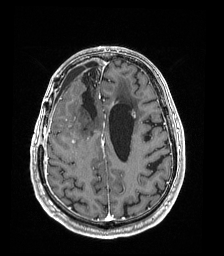
Brain MRI from a brain-tumour surgery series, one axial slice. Position 61 of 192 along the scan axis. T1-weighted post-contrast. 1 mm slice thickness. 224 × 256 image matrix. Case-level facts recorded for this patient, not image findings: histopathology: Astrocytoma; WHO grade: 4.
Outlined on this slice (outlined manually by an expert reader):
- previous resection cavity: bounding box [x1, y1, x2, y2] px = [82, 68, 98, 119]
- tumour: [72, 140, 75, 144]